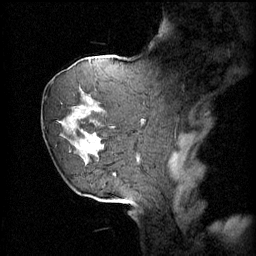
Breast MRI (dynamic contrast-enhanced), one sagittal slice; 4 images stored at this slice position (order not interpretable as contrast timing); 1.5 T; TE 4.2 ms, TR 11 ms; 256 × 256 image matrix, field of view 220 × 220 mm. Female patient, age 72 years.
Outlined on this slice (semi-automatic segmentation, software-assisted and operator-edited):
- analysis volume of interest (the breast-tissue region the enhancement analysis was run in; not a lesion): box from (x=49, y=68) to (x=109, y=163) px
- tumour enhancement mask (voxels above the 70 % enhancement threshold inside the analysis volume of interest): (x=65, y=100)–(x=109, y=149)